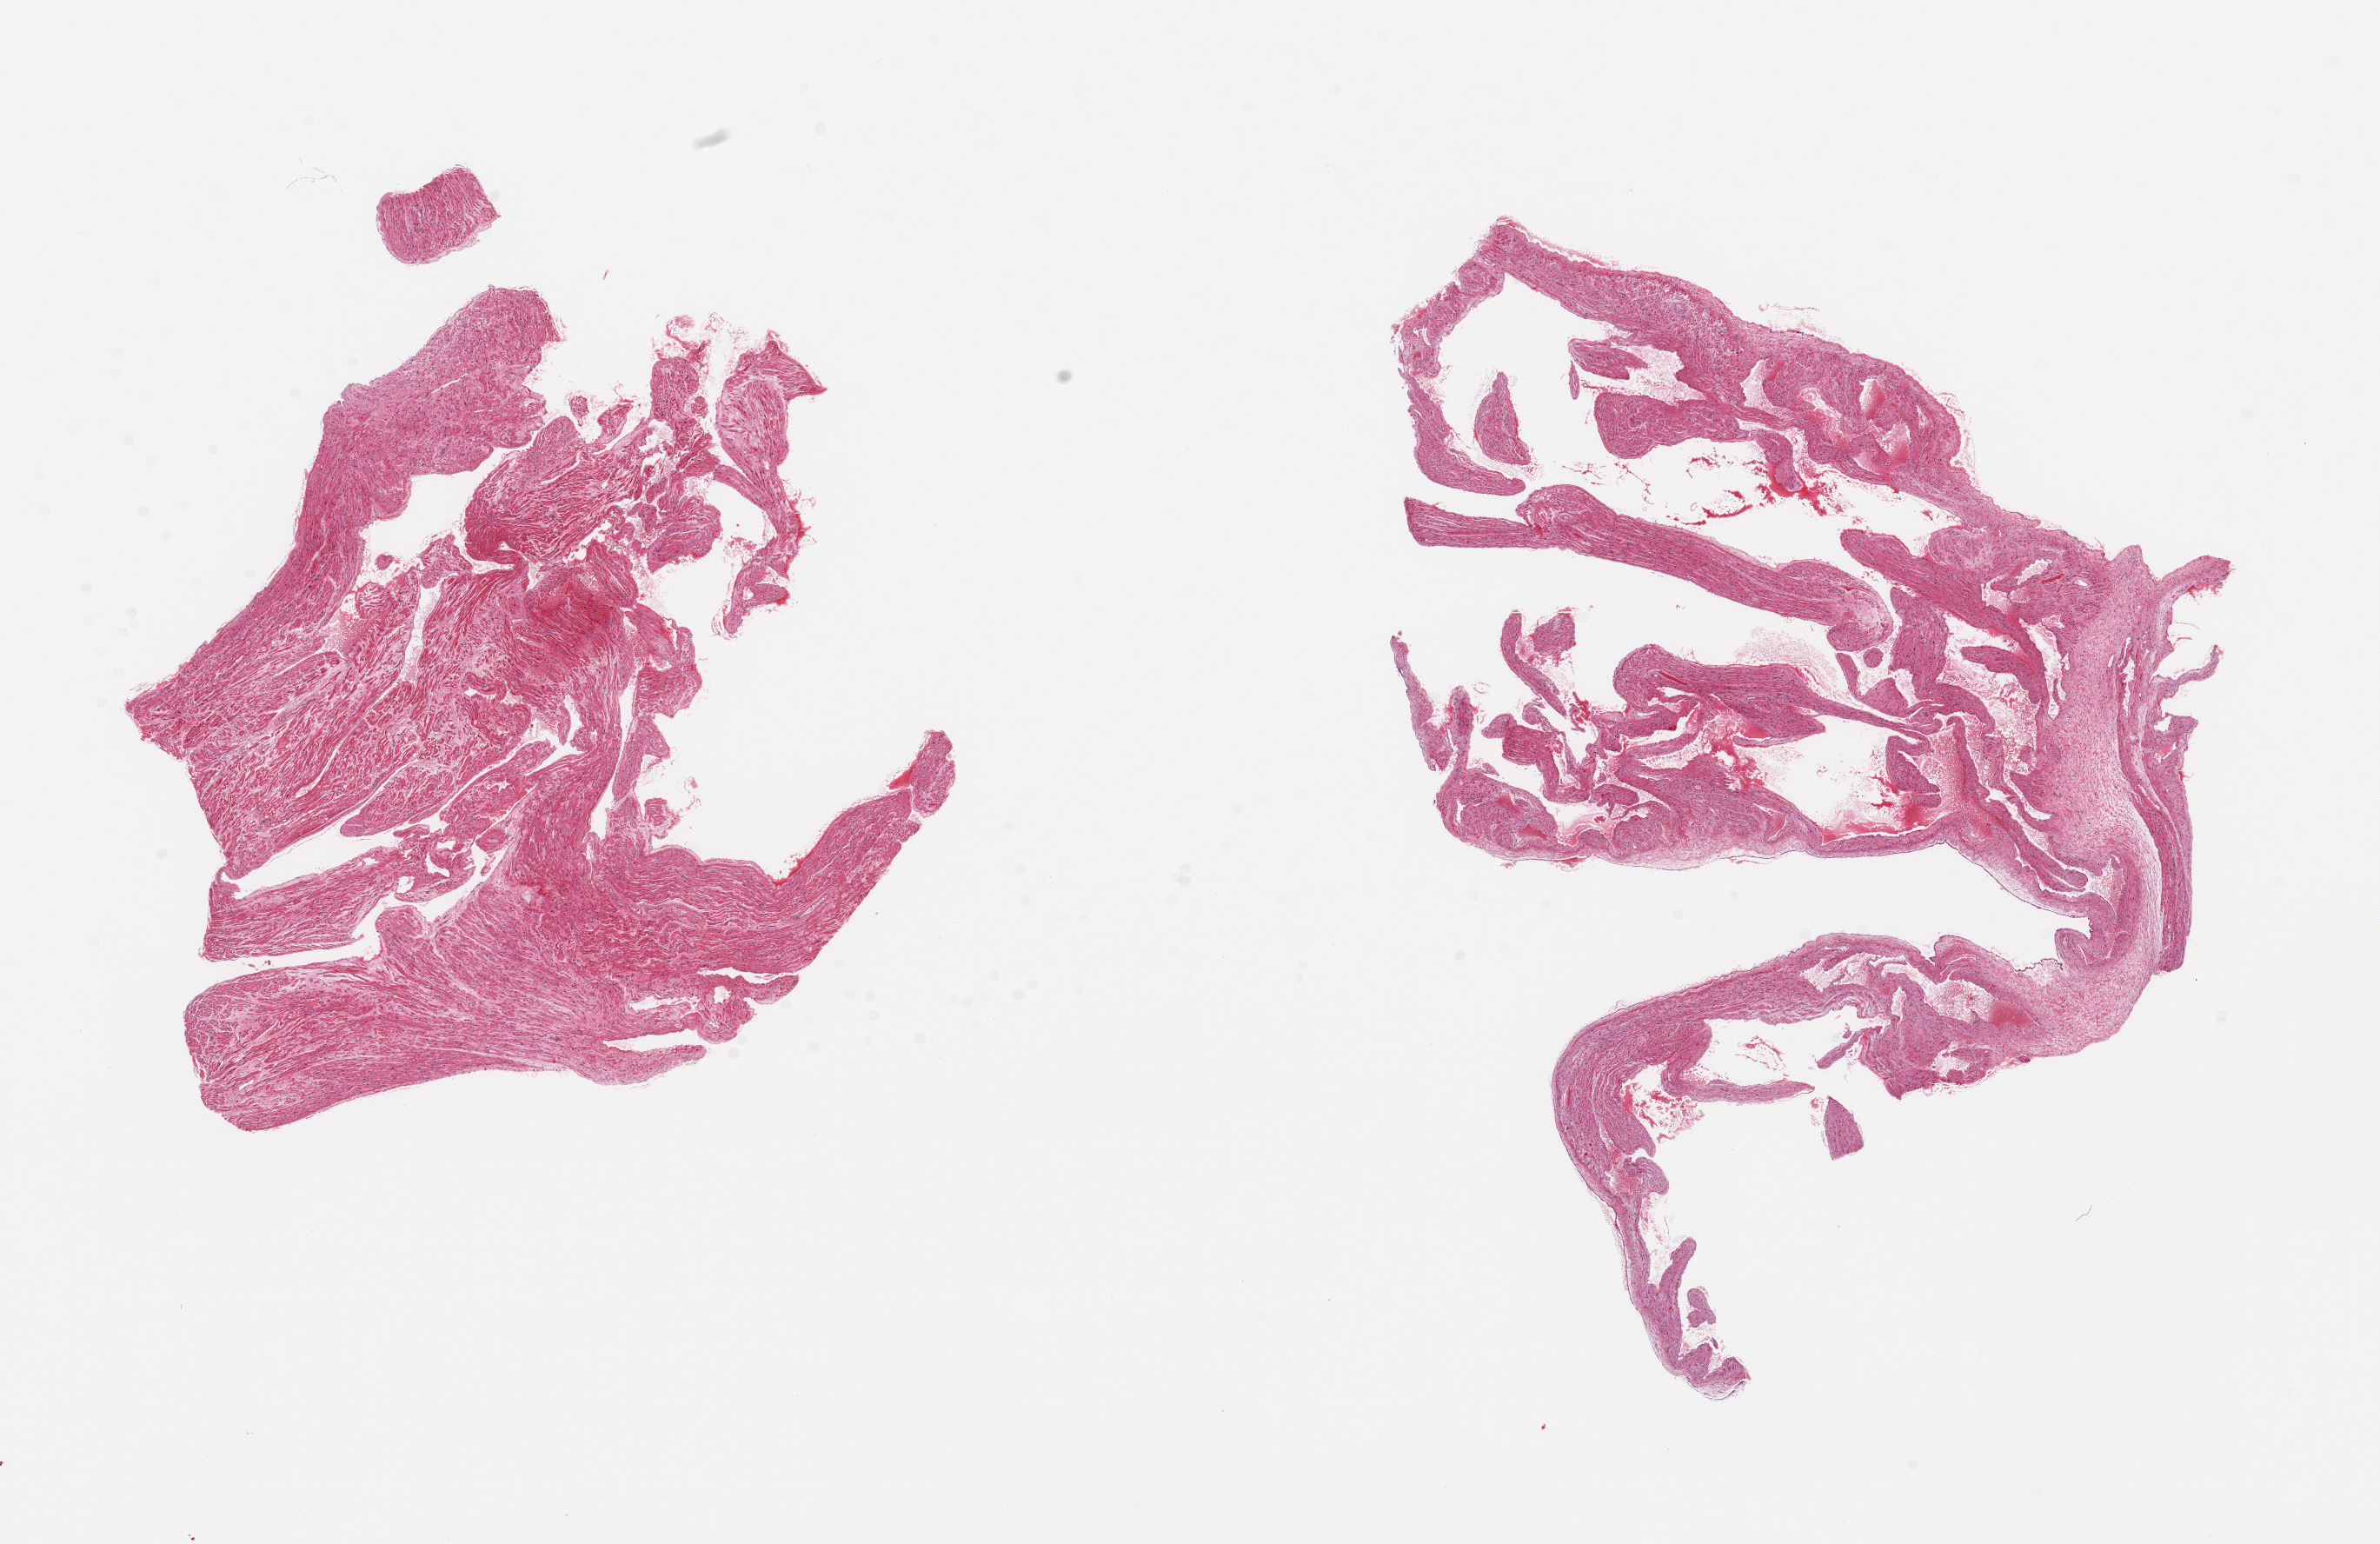
Hematoxylin and eosin (H&E) whole-slide image, brightfield — a low-resolution overview of the entire scanned area, about 21.7 x 14.0 mm (from a 20x scan). PAXgene-fixed paraffin-embedded (PFPE) section. Target tissue: auricular appendage. Tissue donor sample. Donor sex: male.
Review note (as recorded): 2 pieces; no fat; 10% fibrous content in 1.